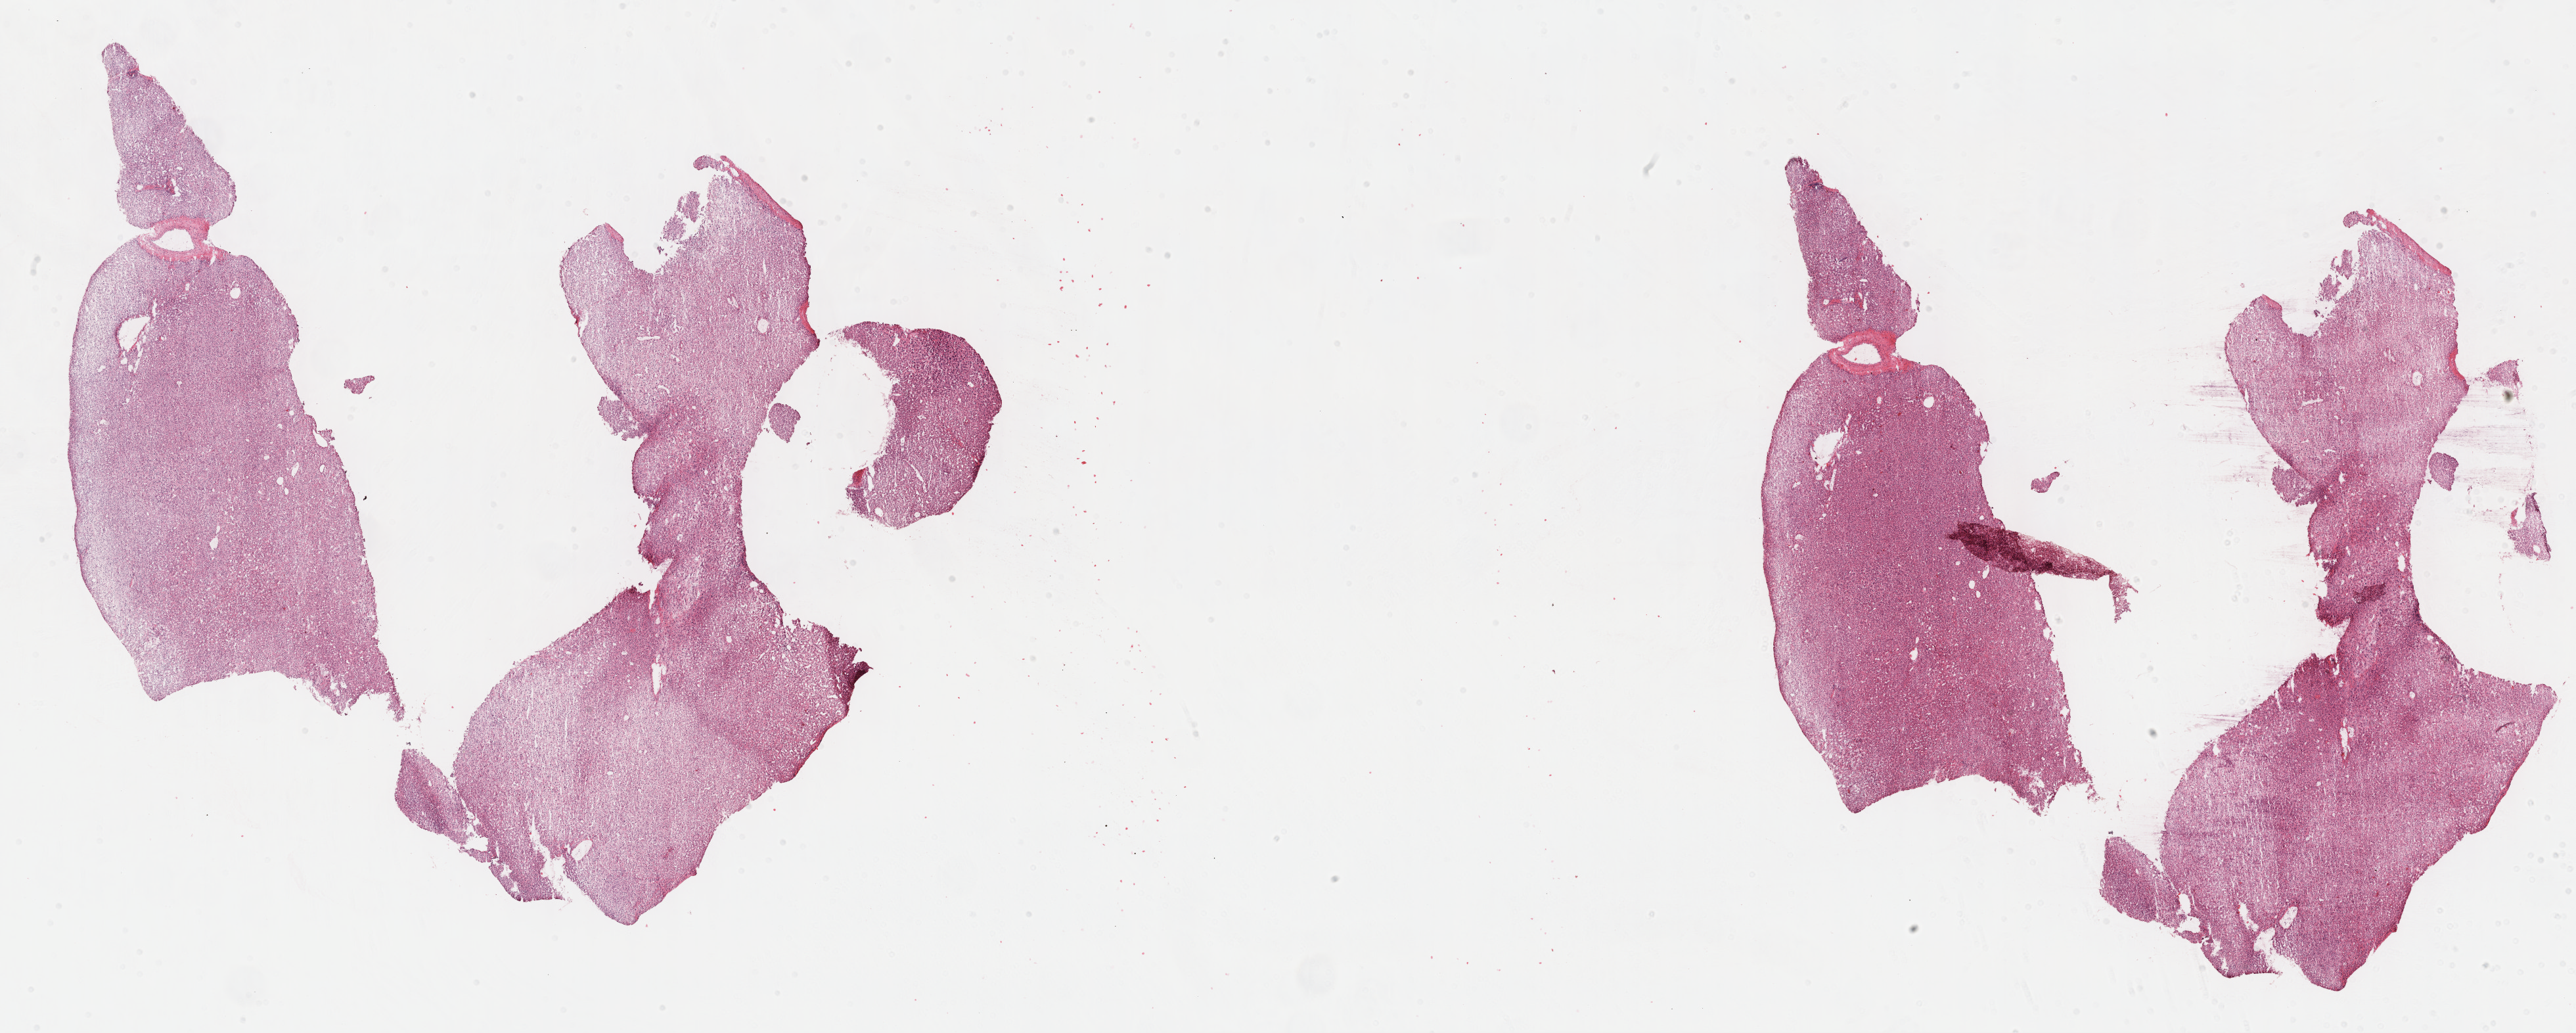
Whole-slide histology image, Hematoxylin and eosin (H&E) stained — shown as a low-resolution overview of the whole scanned area (about 31.7 x 12.7 mm, from a 40x scan); frozen section from the top of the tissue portion; liver, primary tumour sample. Male, age 61 years at initial diagnosis. Histologic grade: G1 (well differentiated). Pathologist review of this section (percent, as recorded): tumour cells 85%, tumour nuclei 85%, normal cells 0%, stromal cells 15%, necrosis 0%. Inflammatory infiltration, as recorded: lymphocyte infiltration 2%, monocyte infiltration 1%, neutrophil infiltration 4%.
AJCC pathologic stage: II (7th edition). Histologic diagnosis: Hepatocellular carcinoma, NOS.